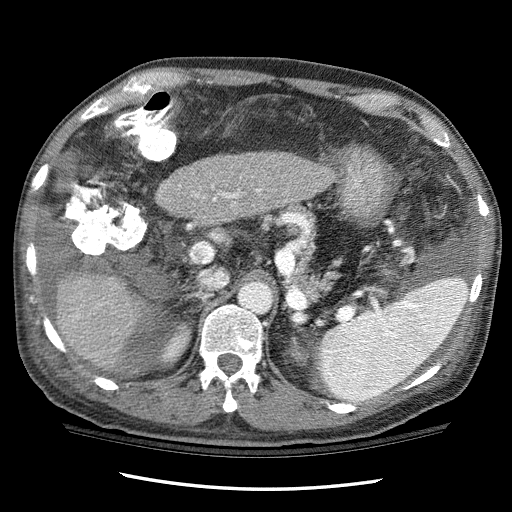
Contrast-enhanced abdominal CT (liver protocol), one axial slice; position 63 of 114 along the scan axis; reconstruction kernel STANDARD; 120 kVp; one of 3 acquisitions stored at this slice position; soft-tissue window (W 400 / L 40 HU); 512 × 512 image matrix, field of view 360 × 360 mm. Case-level facts recorded for this patient, not image findings: diagnosis: hepatocellular carcinoma (patient treated with transarterial chemoembolisation; whether this scan precedes or follows treatment is not stated here); TNM stage (as recorded): Stage-I; Child-Pugh class: C; tumour differentiation: well differentiated.
Structures marked on this image (semi-automatically segmented with operator editing):
- liver parenchyma outside the tumour (the mass and vessels are separate outlines, so this box may not span the whole liver): box from (x=53, y=151) to (x=334, y=368) px
- liver vessels: (x=213, y=189)–(x=260, y=201)